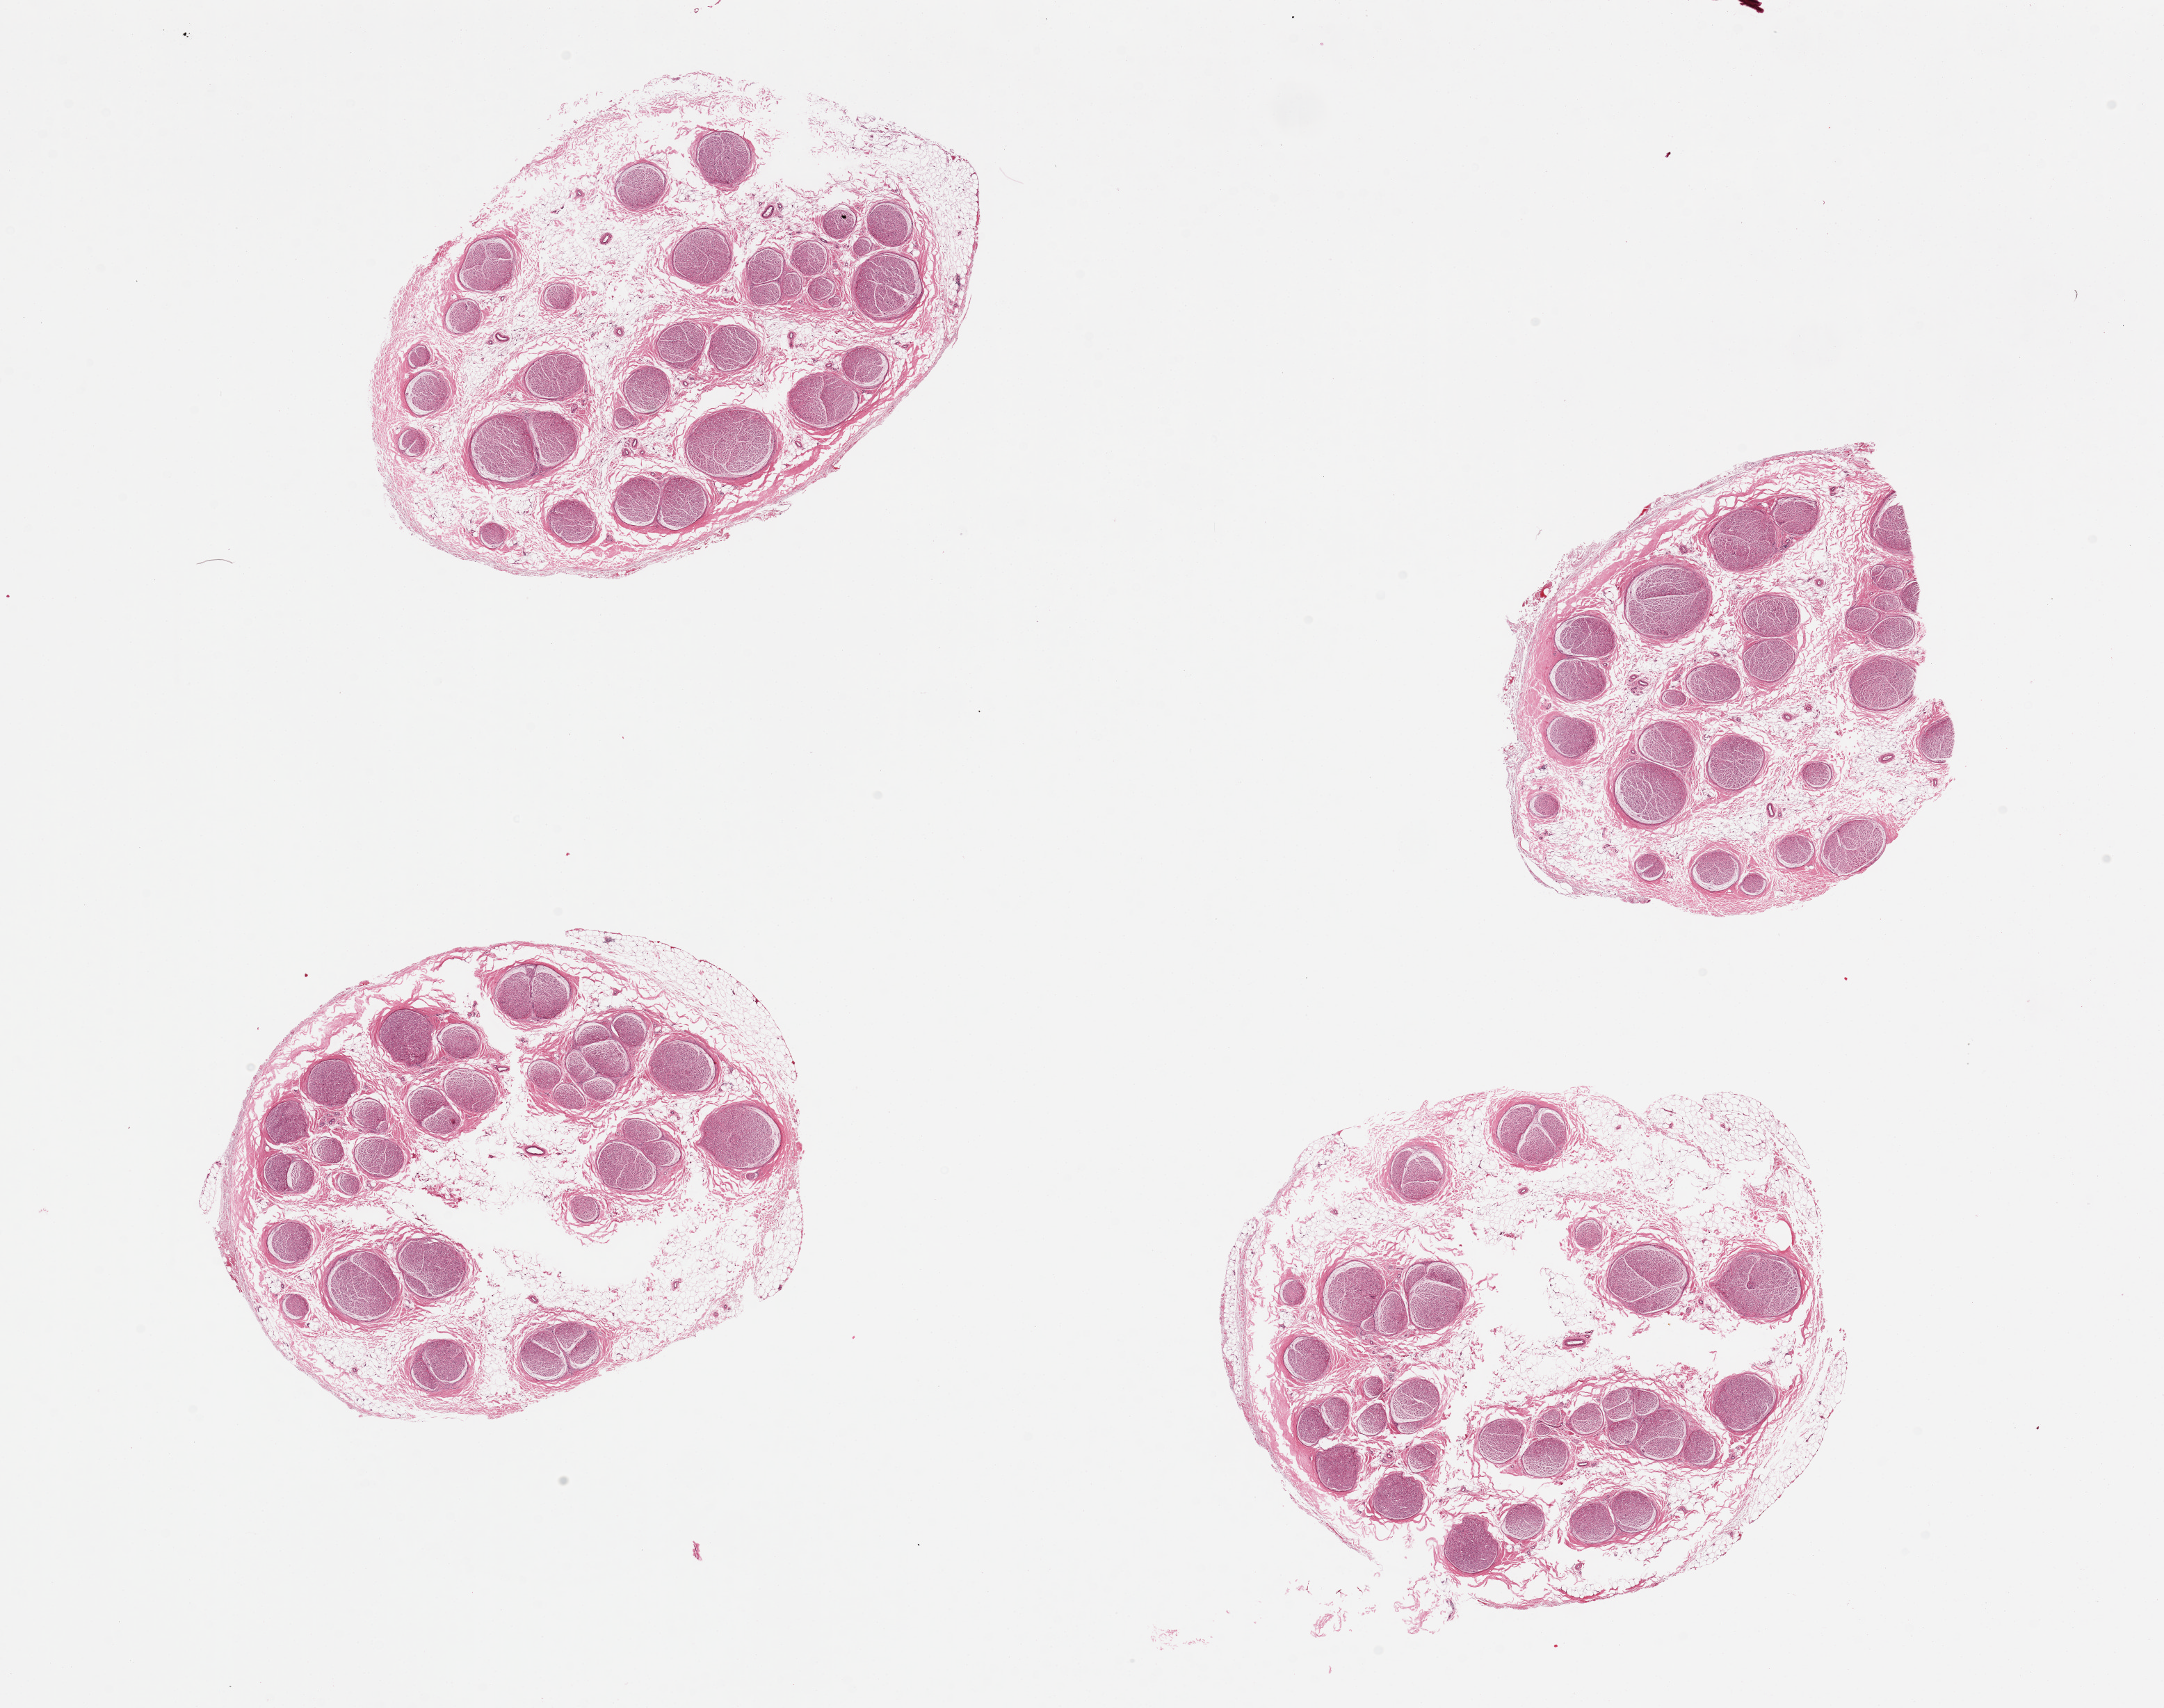
Digitized haematoxylin and eosin-stained section, brightfield, shown as a low-resolution overview of the whole scanned area (about 24.6 x 19.4 mm), PAXgene-fixed, paraffin-embedded tissue, sampled site (target tissue): tibial nerve, donor tissue sample. Donor: female.
• reviewer comment on this tissue sample: 4 pieces, nerve with 30-50% attached and internal fibroadipose tissue, some central defects suggesting incomplete fixation